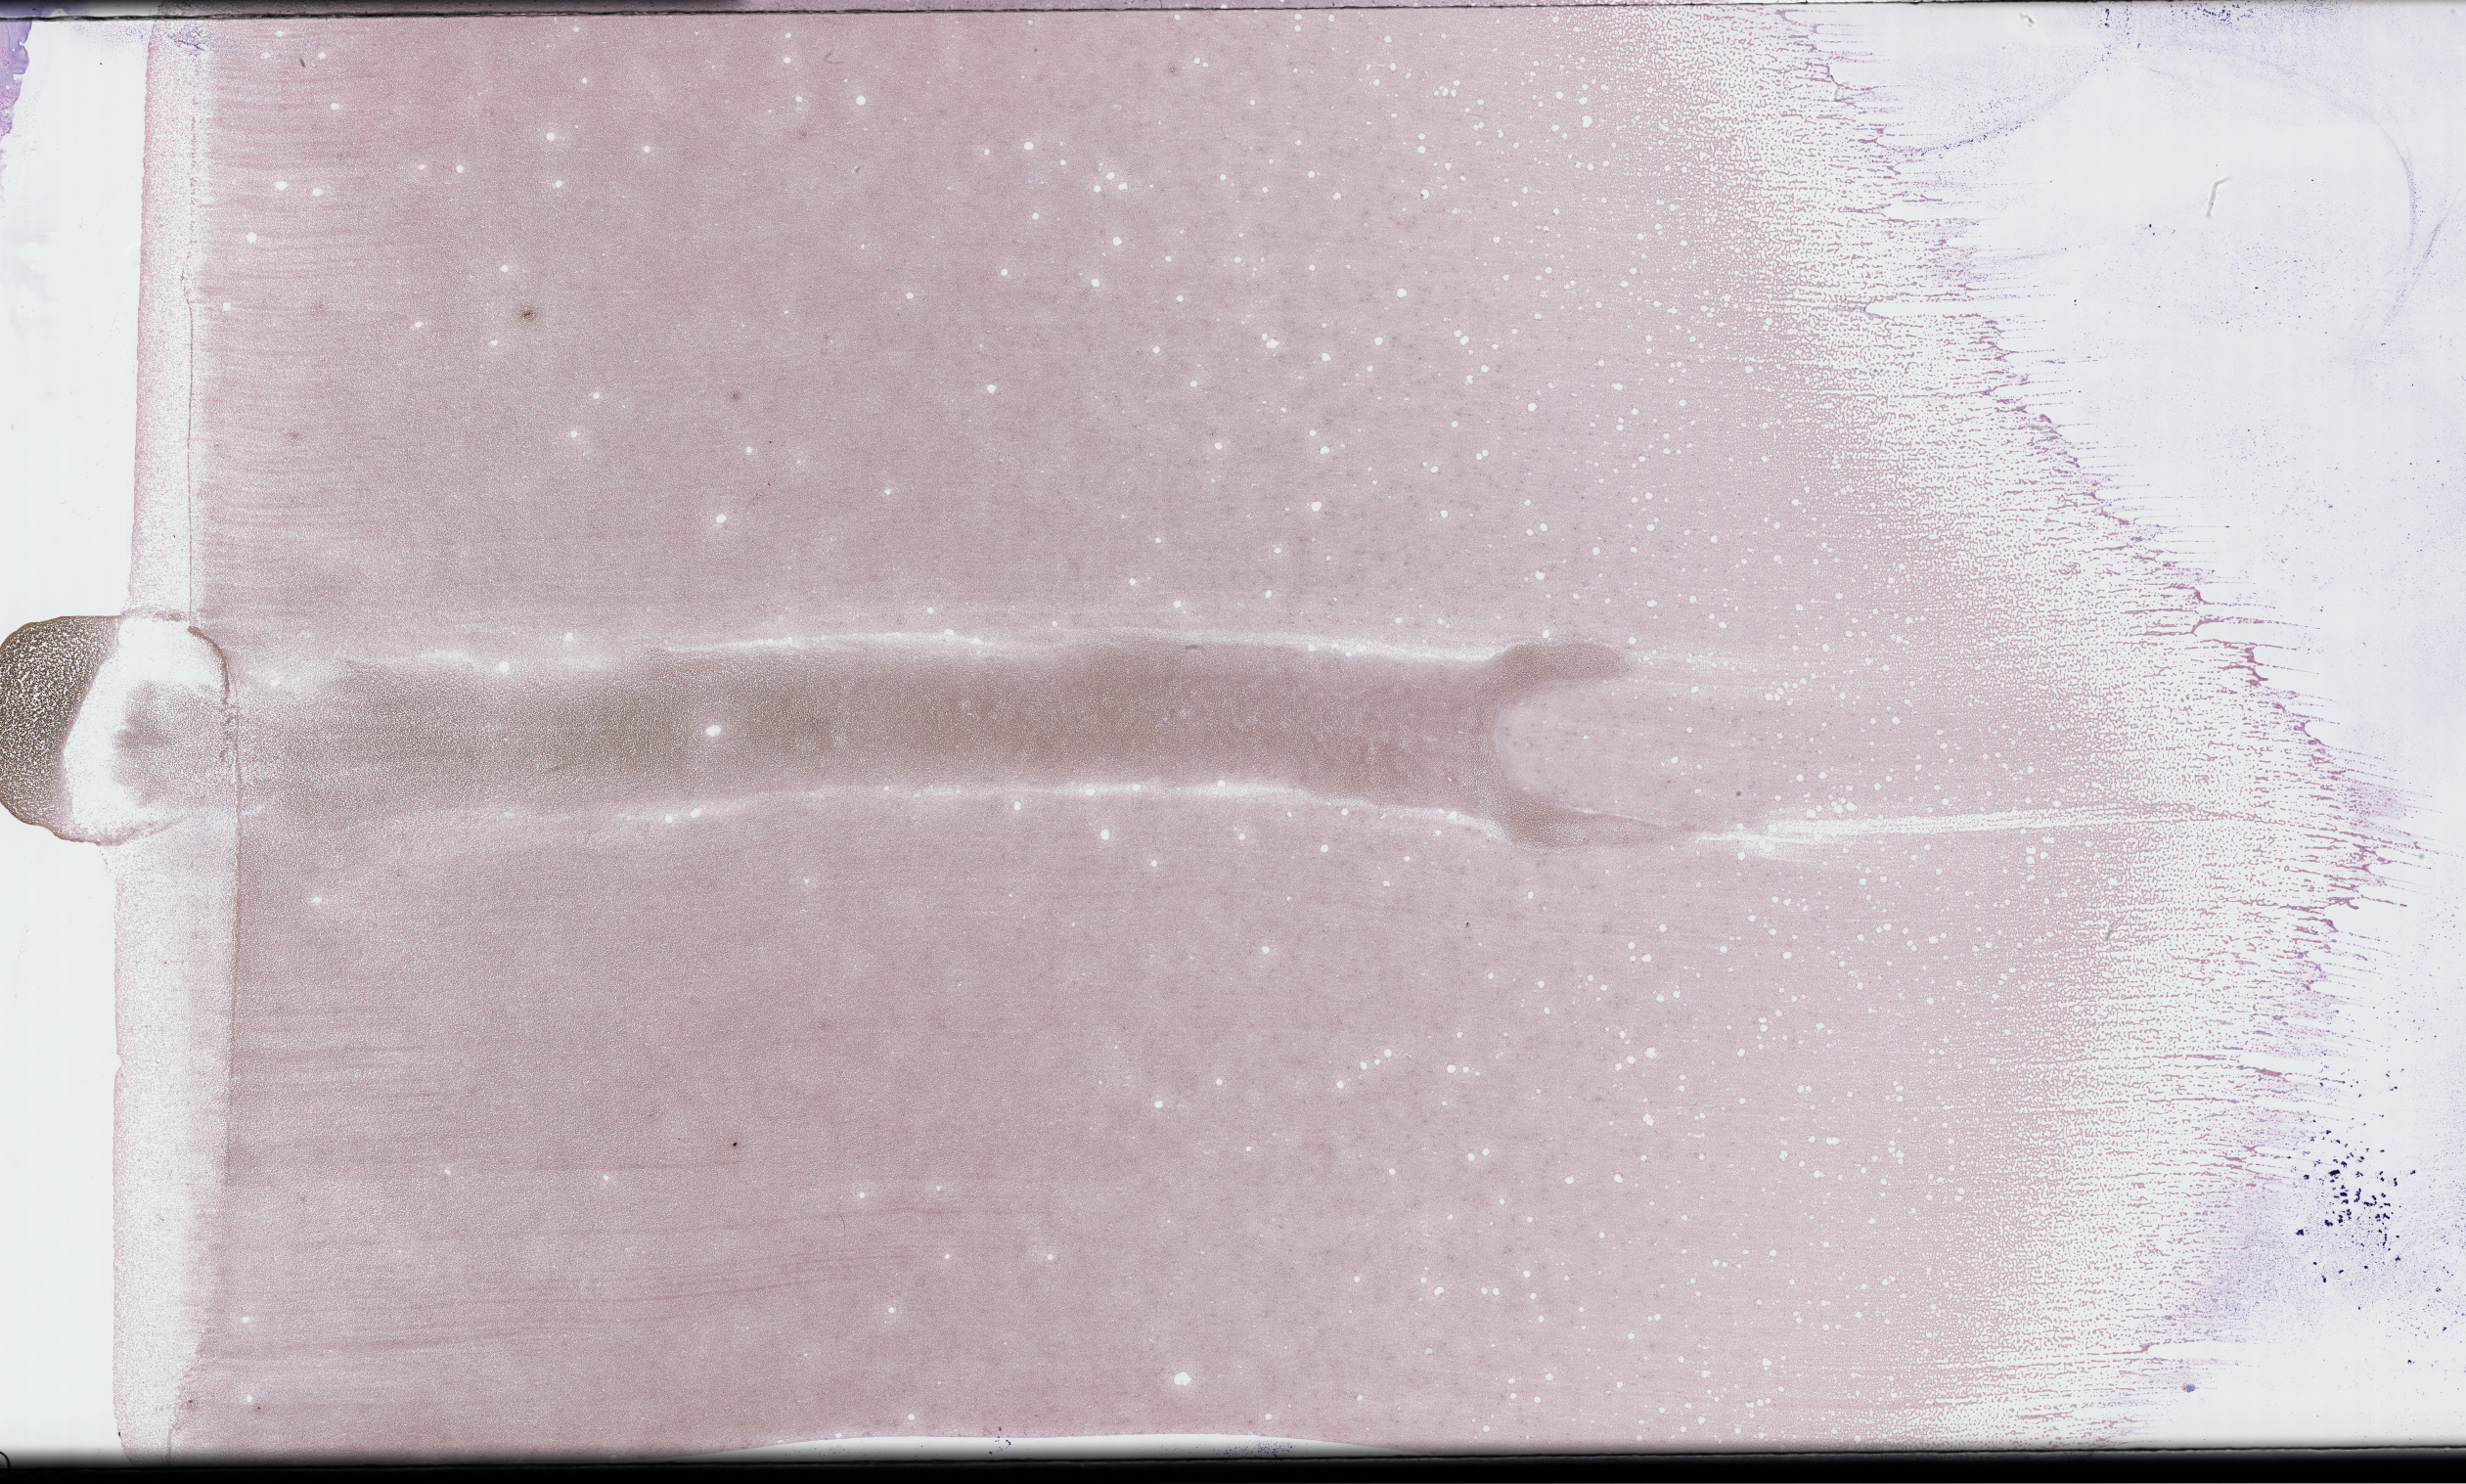
Wright–Giemsa-stained whole blood smear, whole-slide image, low-resolution overview of the scanned area, about 40.7 x 24.5 mm. Patient: male.
• from a patient with: Plasma Cell Myeloma